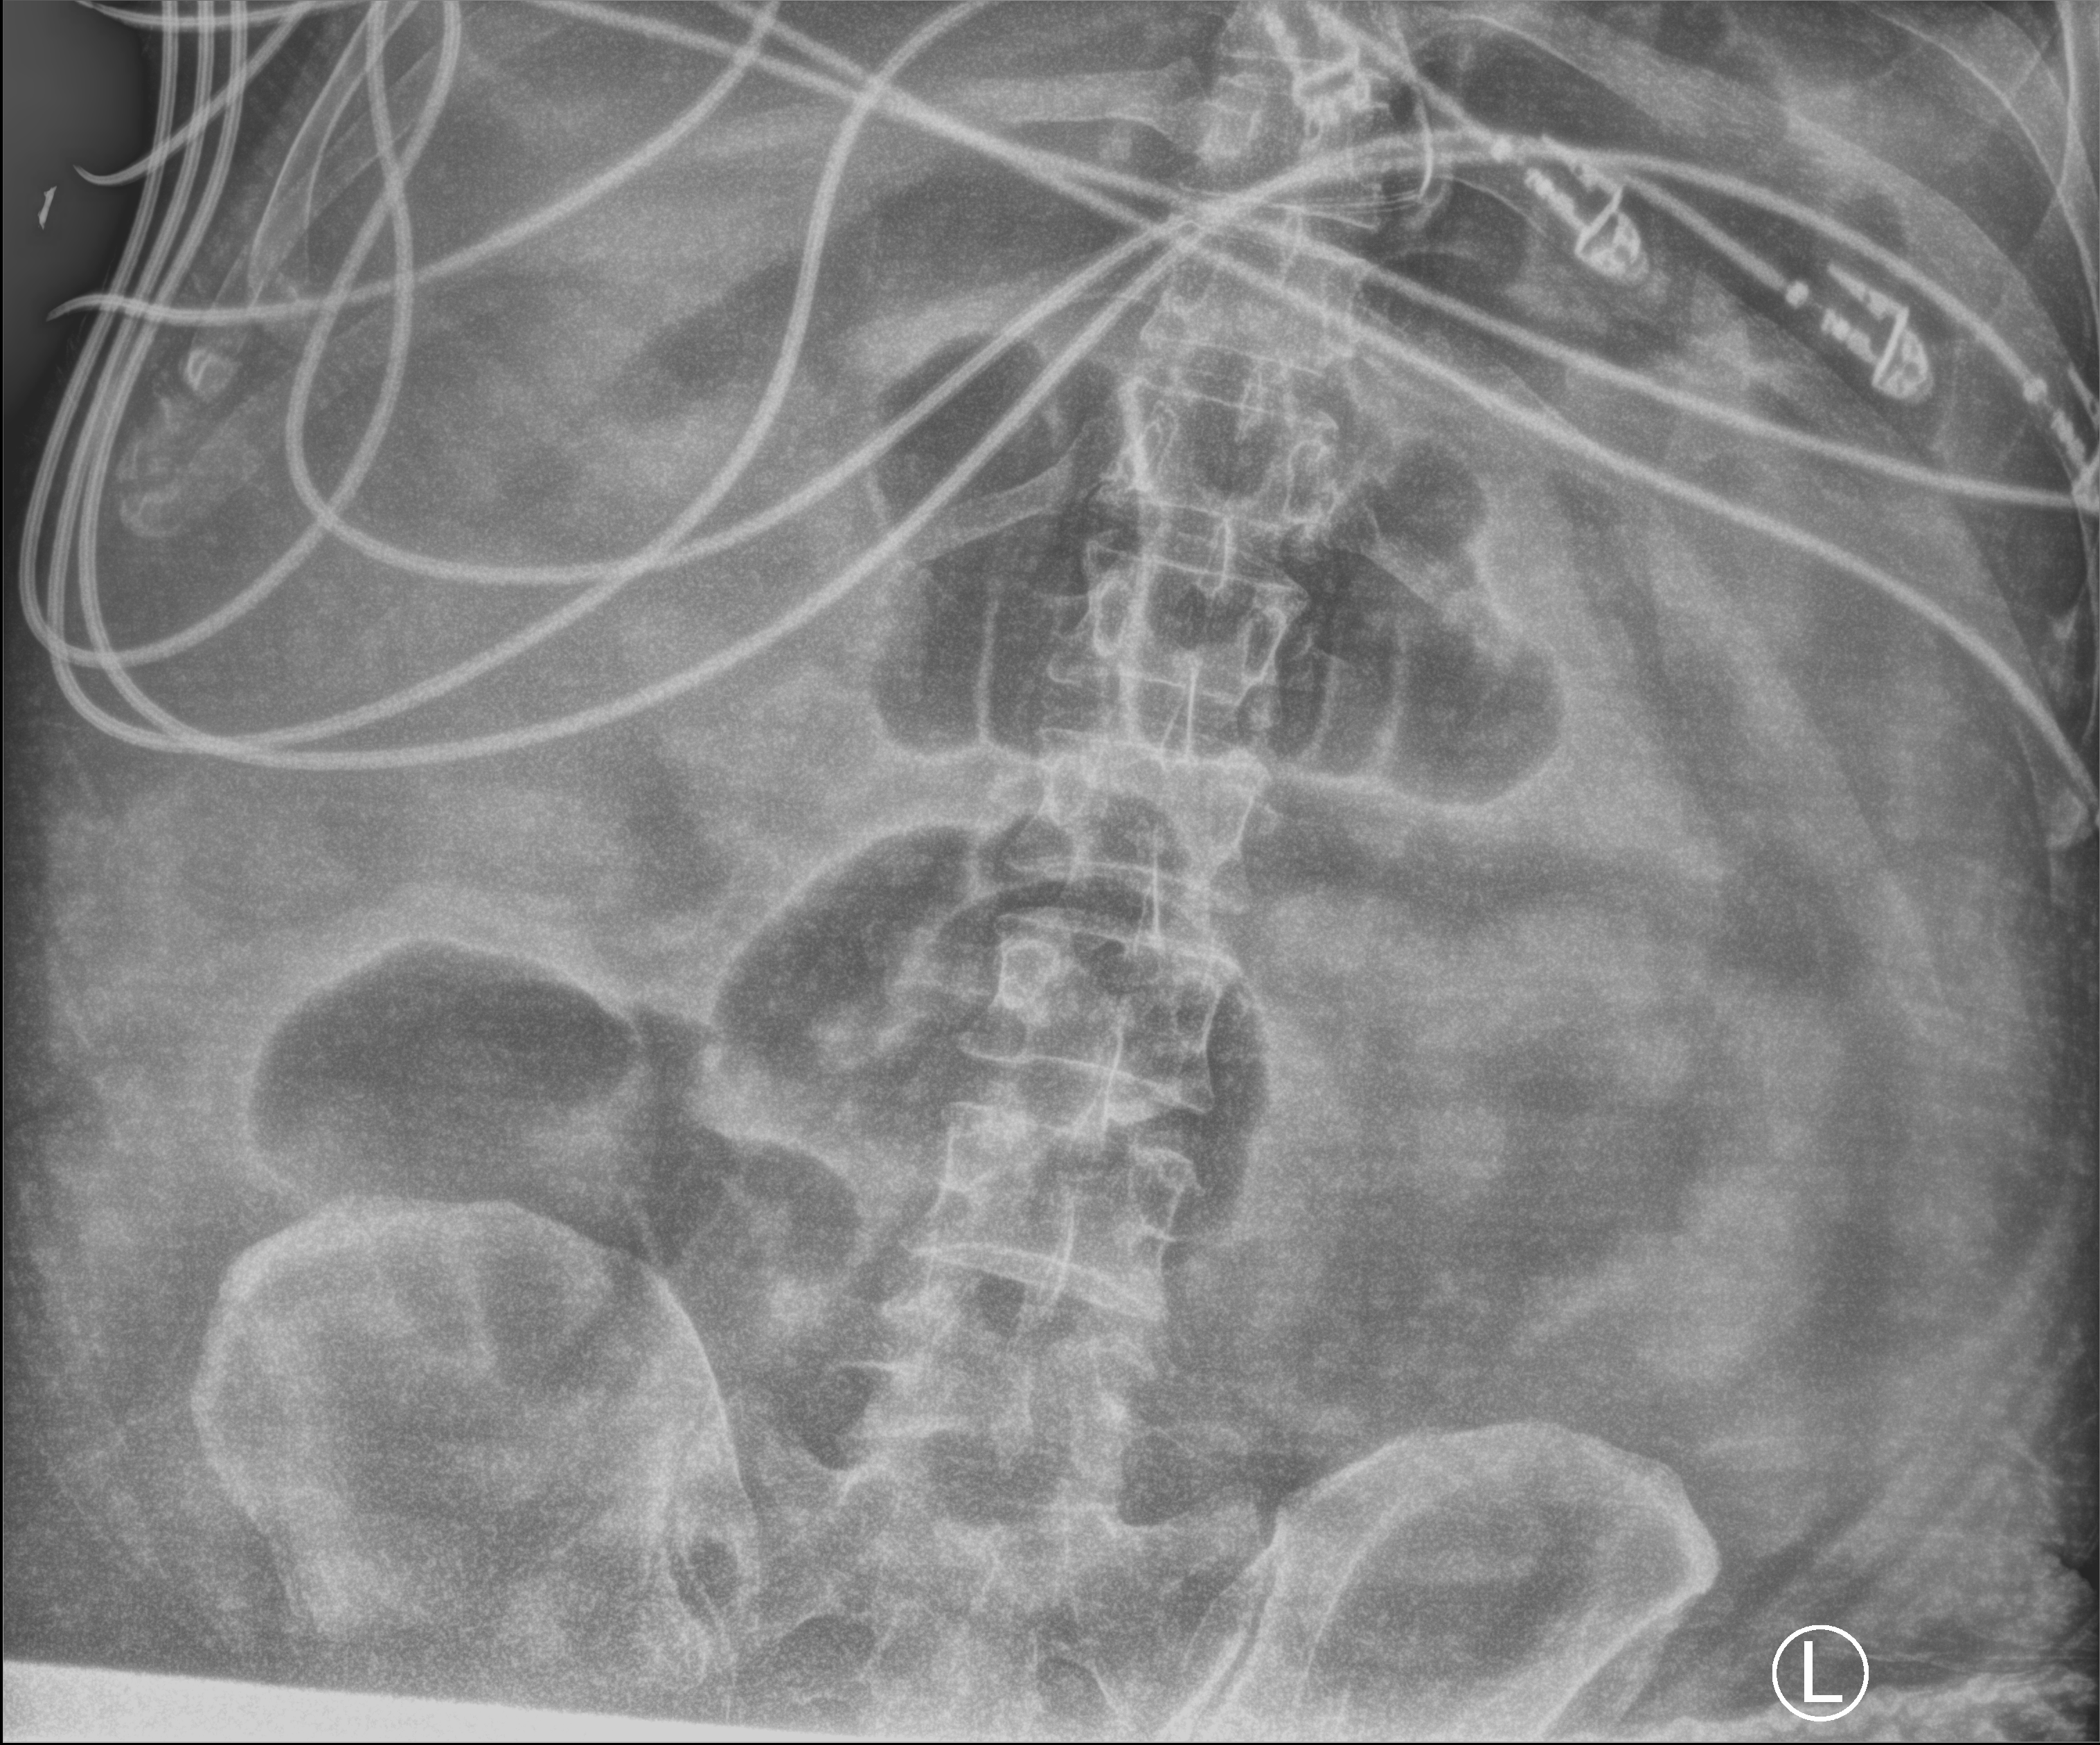
Bedside abdomen radiograph (computed radiography); anteroposterior (AP) projection. Adult patient hospitalised with COVID-19, age 18–59 years.
From the hospital-stay record, not from the radiograph (when in the stay this image was taken is not recorded):
- admitted to intensive care during this hospital stay: yes
- mechanically ventilated during this hospital stay: yes